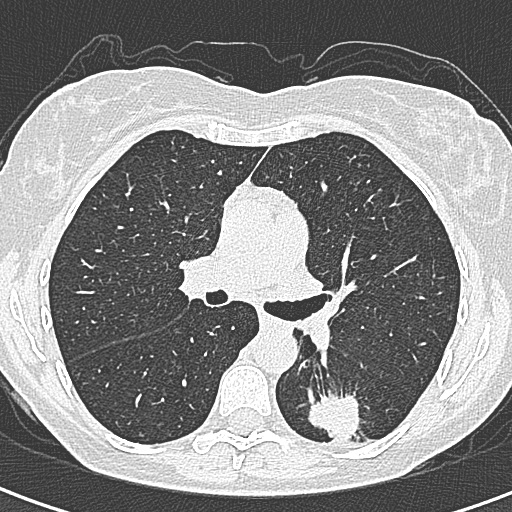
Axial slice from a low-dose chest CT screening exam. First (baseline) screen. Lung window (W 1500 / L -600 HU). 1 mm slice thickness. Lung (sharp) reconstruction kernel (B80f). 120 kVp. Slice 128 of 328 in the series. 512 × 512 image matrix. Female participant, aged 58 years at enrolment. Former smoker at enrolment.
Expert reader's lesion annotation, bounding box <294,388,364,455> (left, top, right, bottom; pixels). The screening reader recorded 2 non-calcified nodules or masses ≥4 mm on this exam (left lower lobe, right lower lobe); which of them this box marks is not recorded. Lung cancer was diagnosed 22 days after this screen: adenocarcinoma, NOS, left lower lobe, moderately differentiated (G2), stage IA (AJCC 6th edition), 25 mm at pathology.